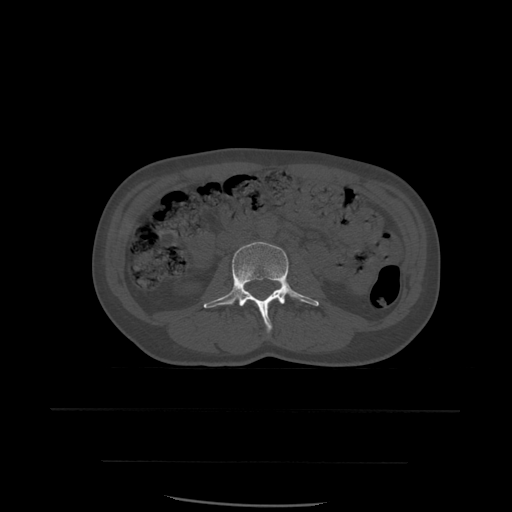
CT including the spine, one axial slice; position 199 of 574 along the scan axis; bone window (W 1800 / L 400 HU); 1.25 mm slice thickness; 512 × 512 image matrix. Patient age 48 years. Case-level facts recorded for this patient, not image findings: primary cancer: lung; vertebrae with lytic lesions (as recorded): T11.
Structures marked on this image (semi-automatic segmentation, software-assisted and operator-edited):
- L3 vertebra: box from (x=204, y=242) to (x=320, y=333) px